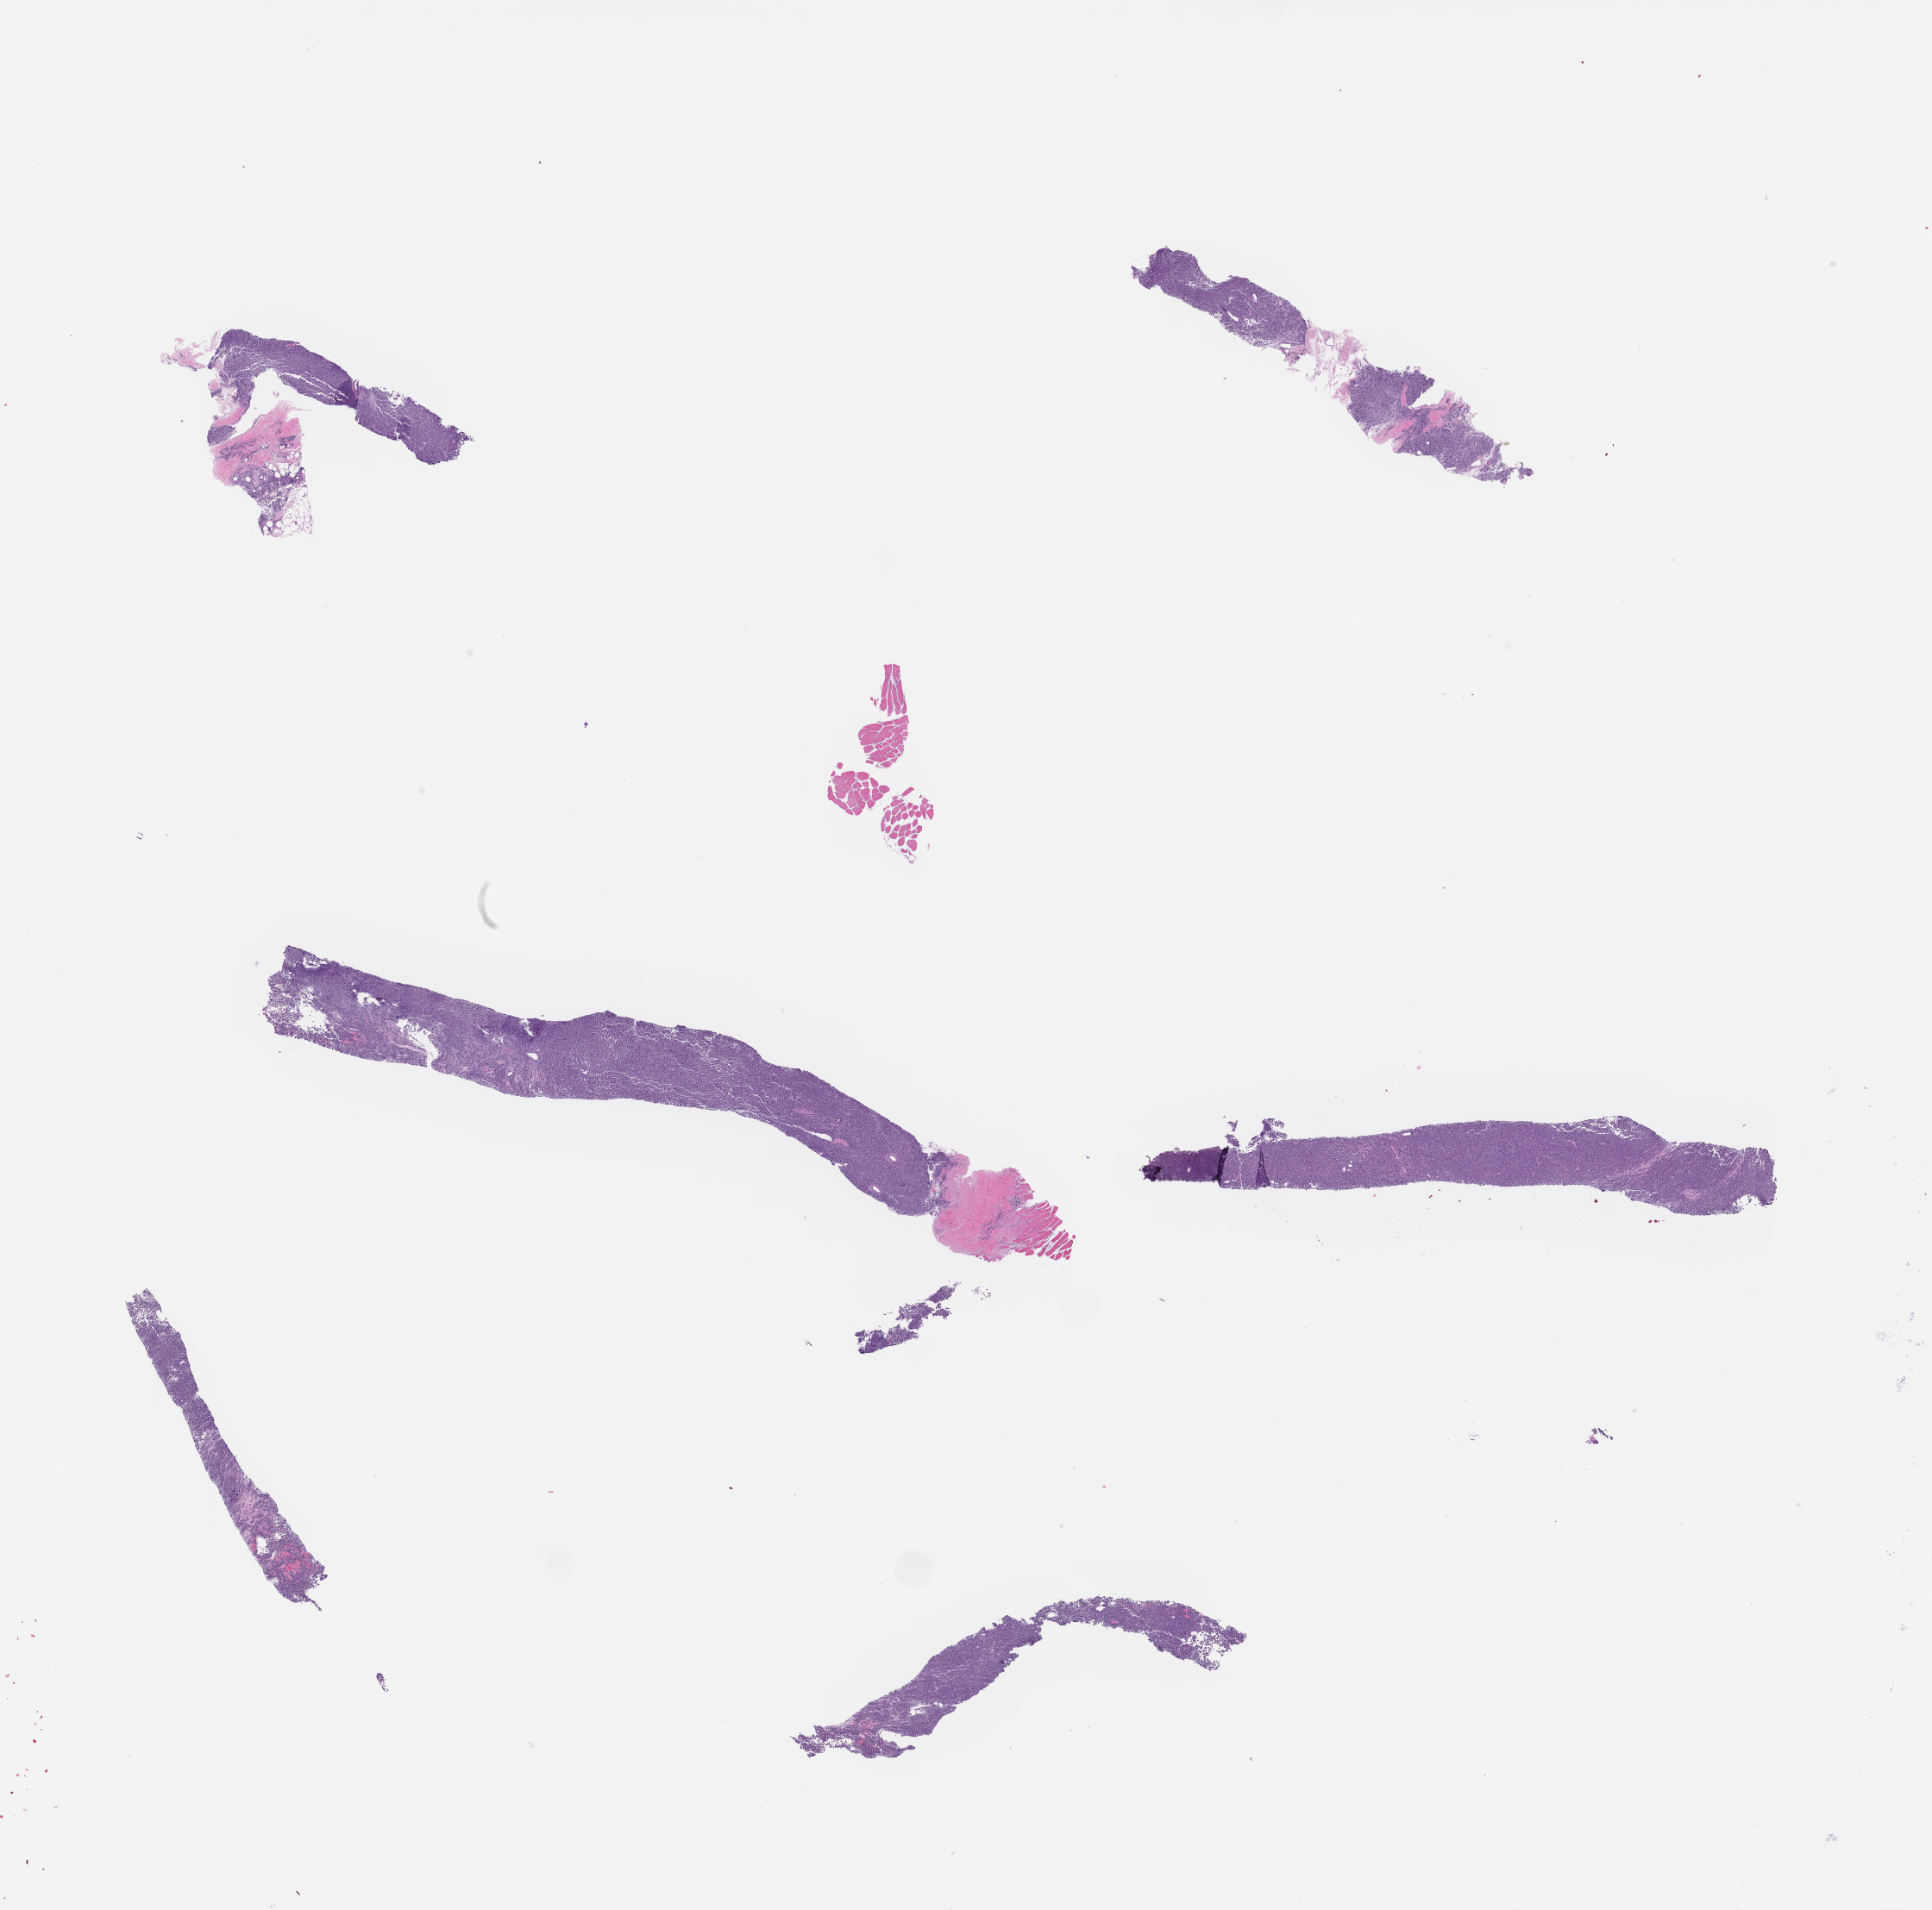
Haematoxylin and eosin whole-slide image, whole scanned area (about 18.1 x 17.9 mm) shown as a low-resolution overview, formalin-fixed paraffin-embedded section, site: bone marrow, specimen time point: collected at baseline (before treatment). Patient sex: male.
This section: primary tumor. Diagnosis: Plasma Cell Myeloma.